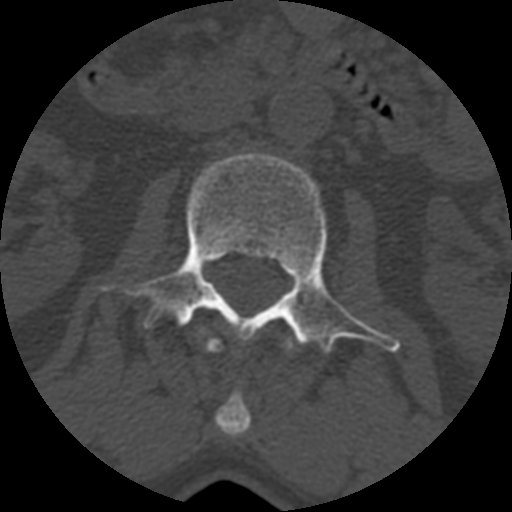
CT including the spine, one axial slice. Bone window (W 1800 / L 400 HU). 1.25 mm slice thickness. 512 × 512 image matrix, field of view 160 × 160 mm. Patient age 71 years. From the clinical record (not read from this slice): primary cancer: prostate.
Outlined on this slice (semi-automatically segmented with operator editing):
- L1 vertebra: bounding box <205,338,293,437> (left, top, right, bottom; pixels)
- L2 vertebra: <99,152,401,352>